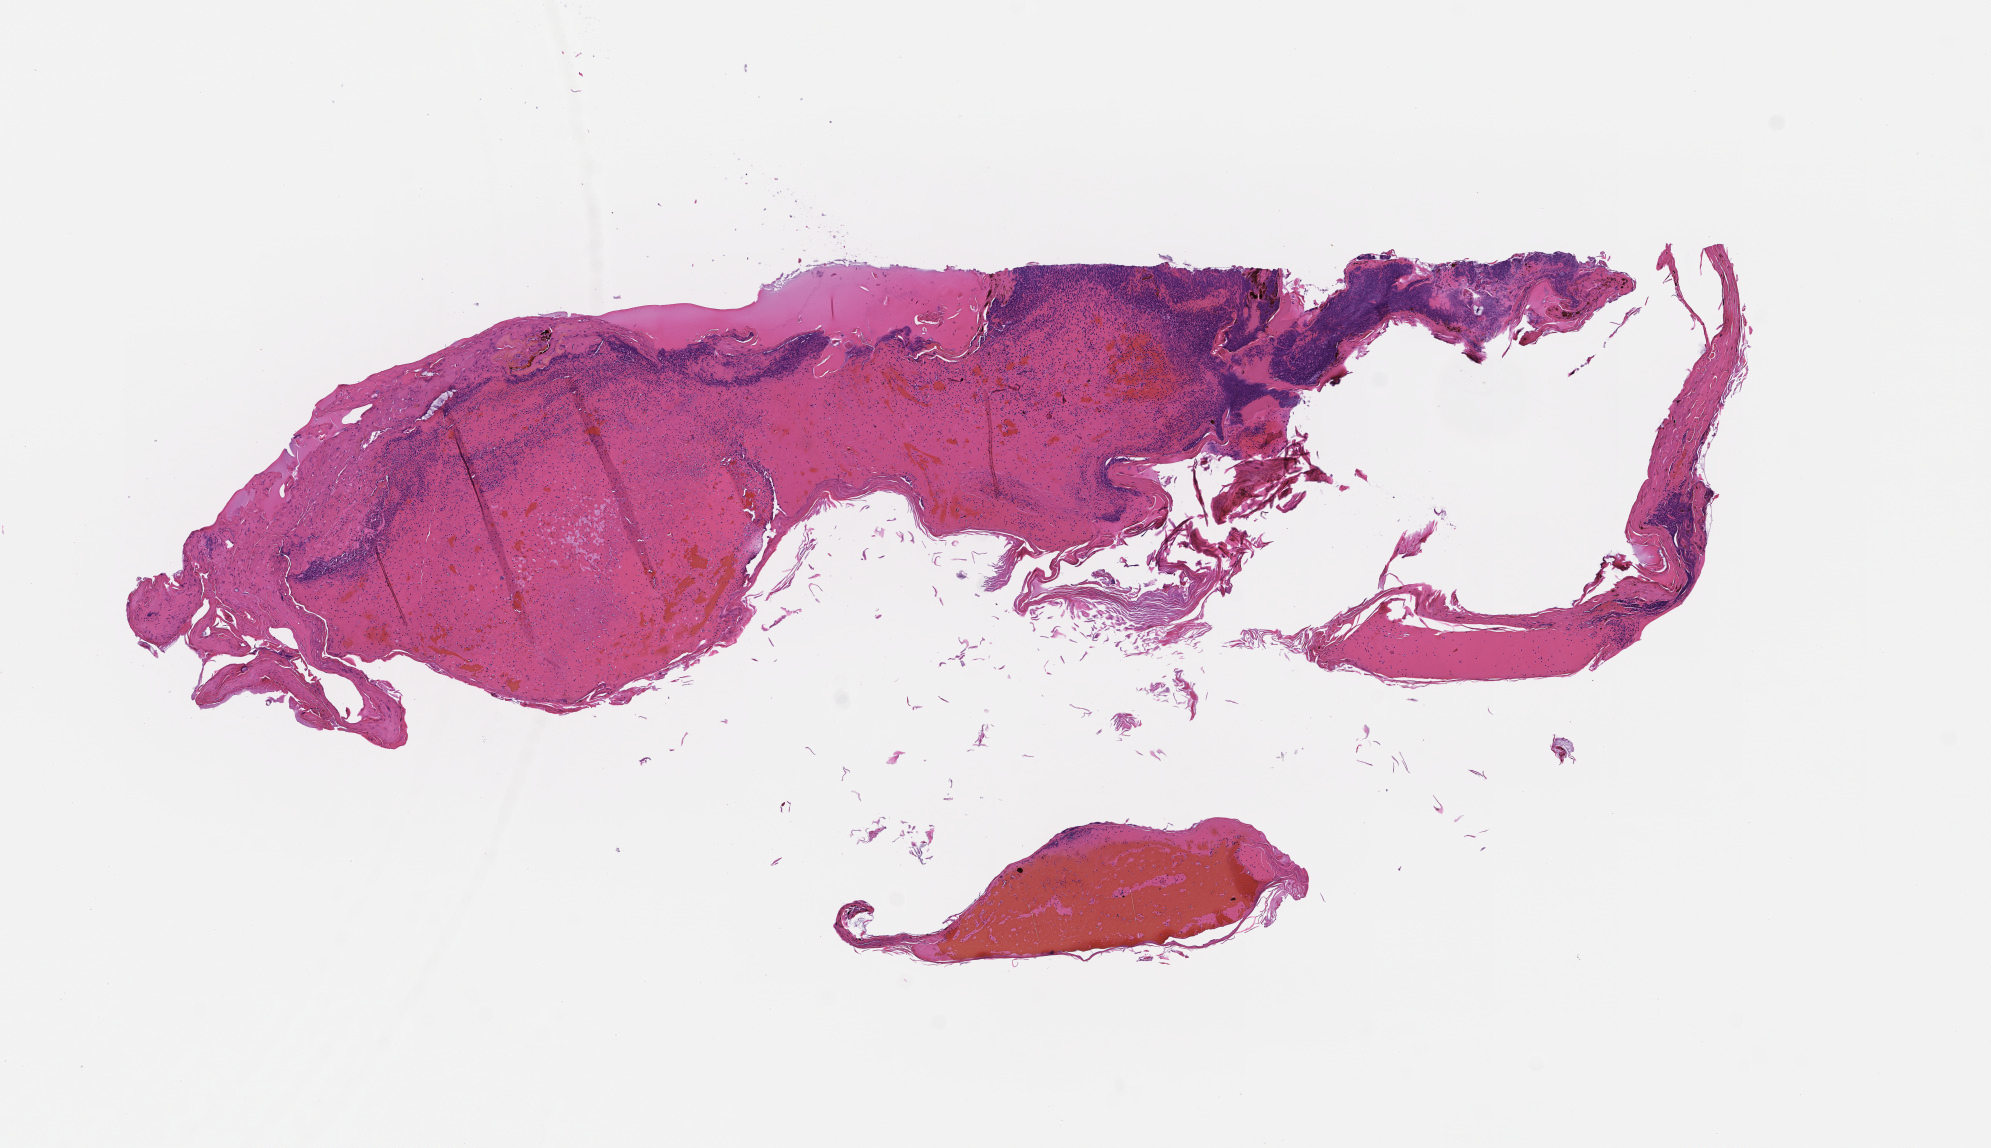
Whole-slide image, hematoxylin and eosin (H&E) stain — whole scanned area (about 8.0 x 4.6 mm) shown as a low-resolution overview; FFPE section; site: skin. Patient sex: male.
- this section: primary tumor
- diagnosis: Melanoma